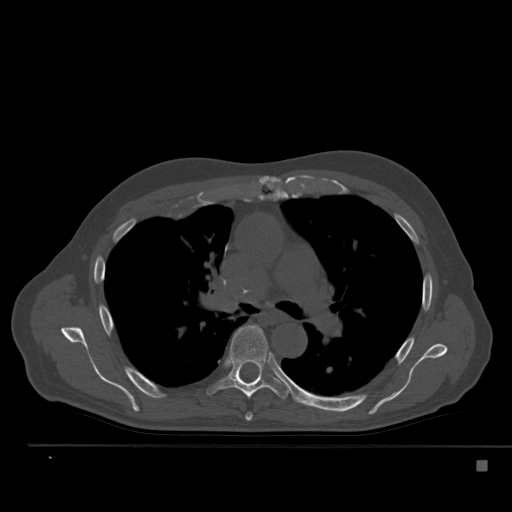
CT including the spine, one axial slice; slice 350 of 517 in the series (ordered by position); reconstruction kernel Br40s; 120 kVp; bone window (W 1800 / L 400 HU); 1.5 mm slice thickness; 512 × 512 image matrix, field of view 408 × 408 mm. Patient: male, 70 years. Case-level facts recorded for this patient, not image findings: primary cancer: renal.
Structures marked on this image (semi-automatic segmentation, software-assisted and operator-edited):
- T5 vertebra: bounding box <245,413,253,421> (left, top, right, bottom; pixels)
- T6 vertebra: <207,325,290,399>